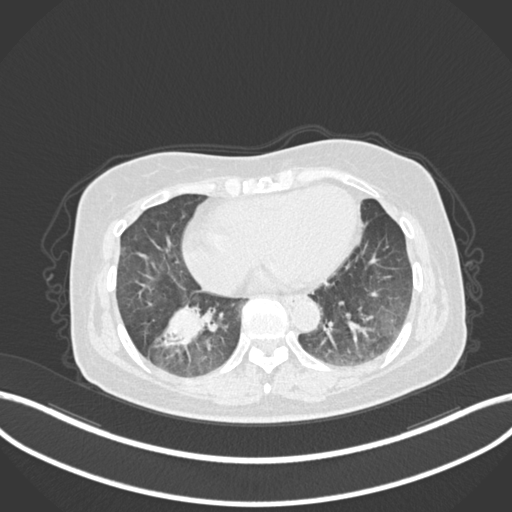
Chest CT, one axial slice. Position 45 of 222 along the scan axis. Reconstruction kernel B30f. 120 kVp. Lung window (W 1500 / L -600 HU). 512 × 512 image matrix, field of view 400 × 400 mm. Female patient, age 67 years. Case-level facts recorded for this patient, not image findings: clinical TNM (as recorded): T1c N1 M0; histopathological grade: G2-3.
Structures marked on this image (rectangle marked by the reading radiologist):
- lung tumour (recorded histology: adenocarcinoma): bounding box <150,292,219,353> (left, top, right, bottom; pixels)